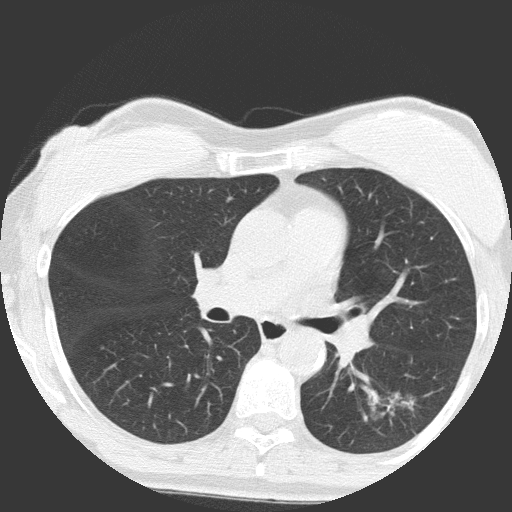
Axial slice from a low-dose chest CT screening exam; baseline screening round; lung window (W 1500 / L -600 HU); 120 kVp; slice 63 of 149 in the series. Female, age 64 years at enrolment. Former smoker at enrolment.
Lesion marked by an expert reader, box from (x=352, y=378) to (x=436, y=453) px. Reader record for this screening exam (exam-level; its link to the box is not recorded): non-calcified nodule or mass ≥4 mm, right upper lobe, 4 × 4 mm, poorly defined margins, ground glass attenuation. Note: the box lies in the patient's left hemithorax on this image, whereas the reader's record names the right lung; they may be different findings. Official screen result: positive, change unspecified: nodule(s) >= 4 mm or enlarging nodule(s), mass(es), or other non-specific abnormalities suspicious for lung cancer. Later outcome: lung cancer diagnosed 932 days after this screen — adenocarcinoma, NOS, left lower lobe, moderately differentiated (G2), stage IA (AJCC 6th edition), 17 mm at pathology.